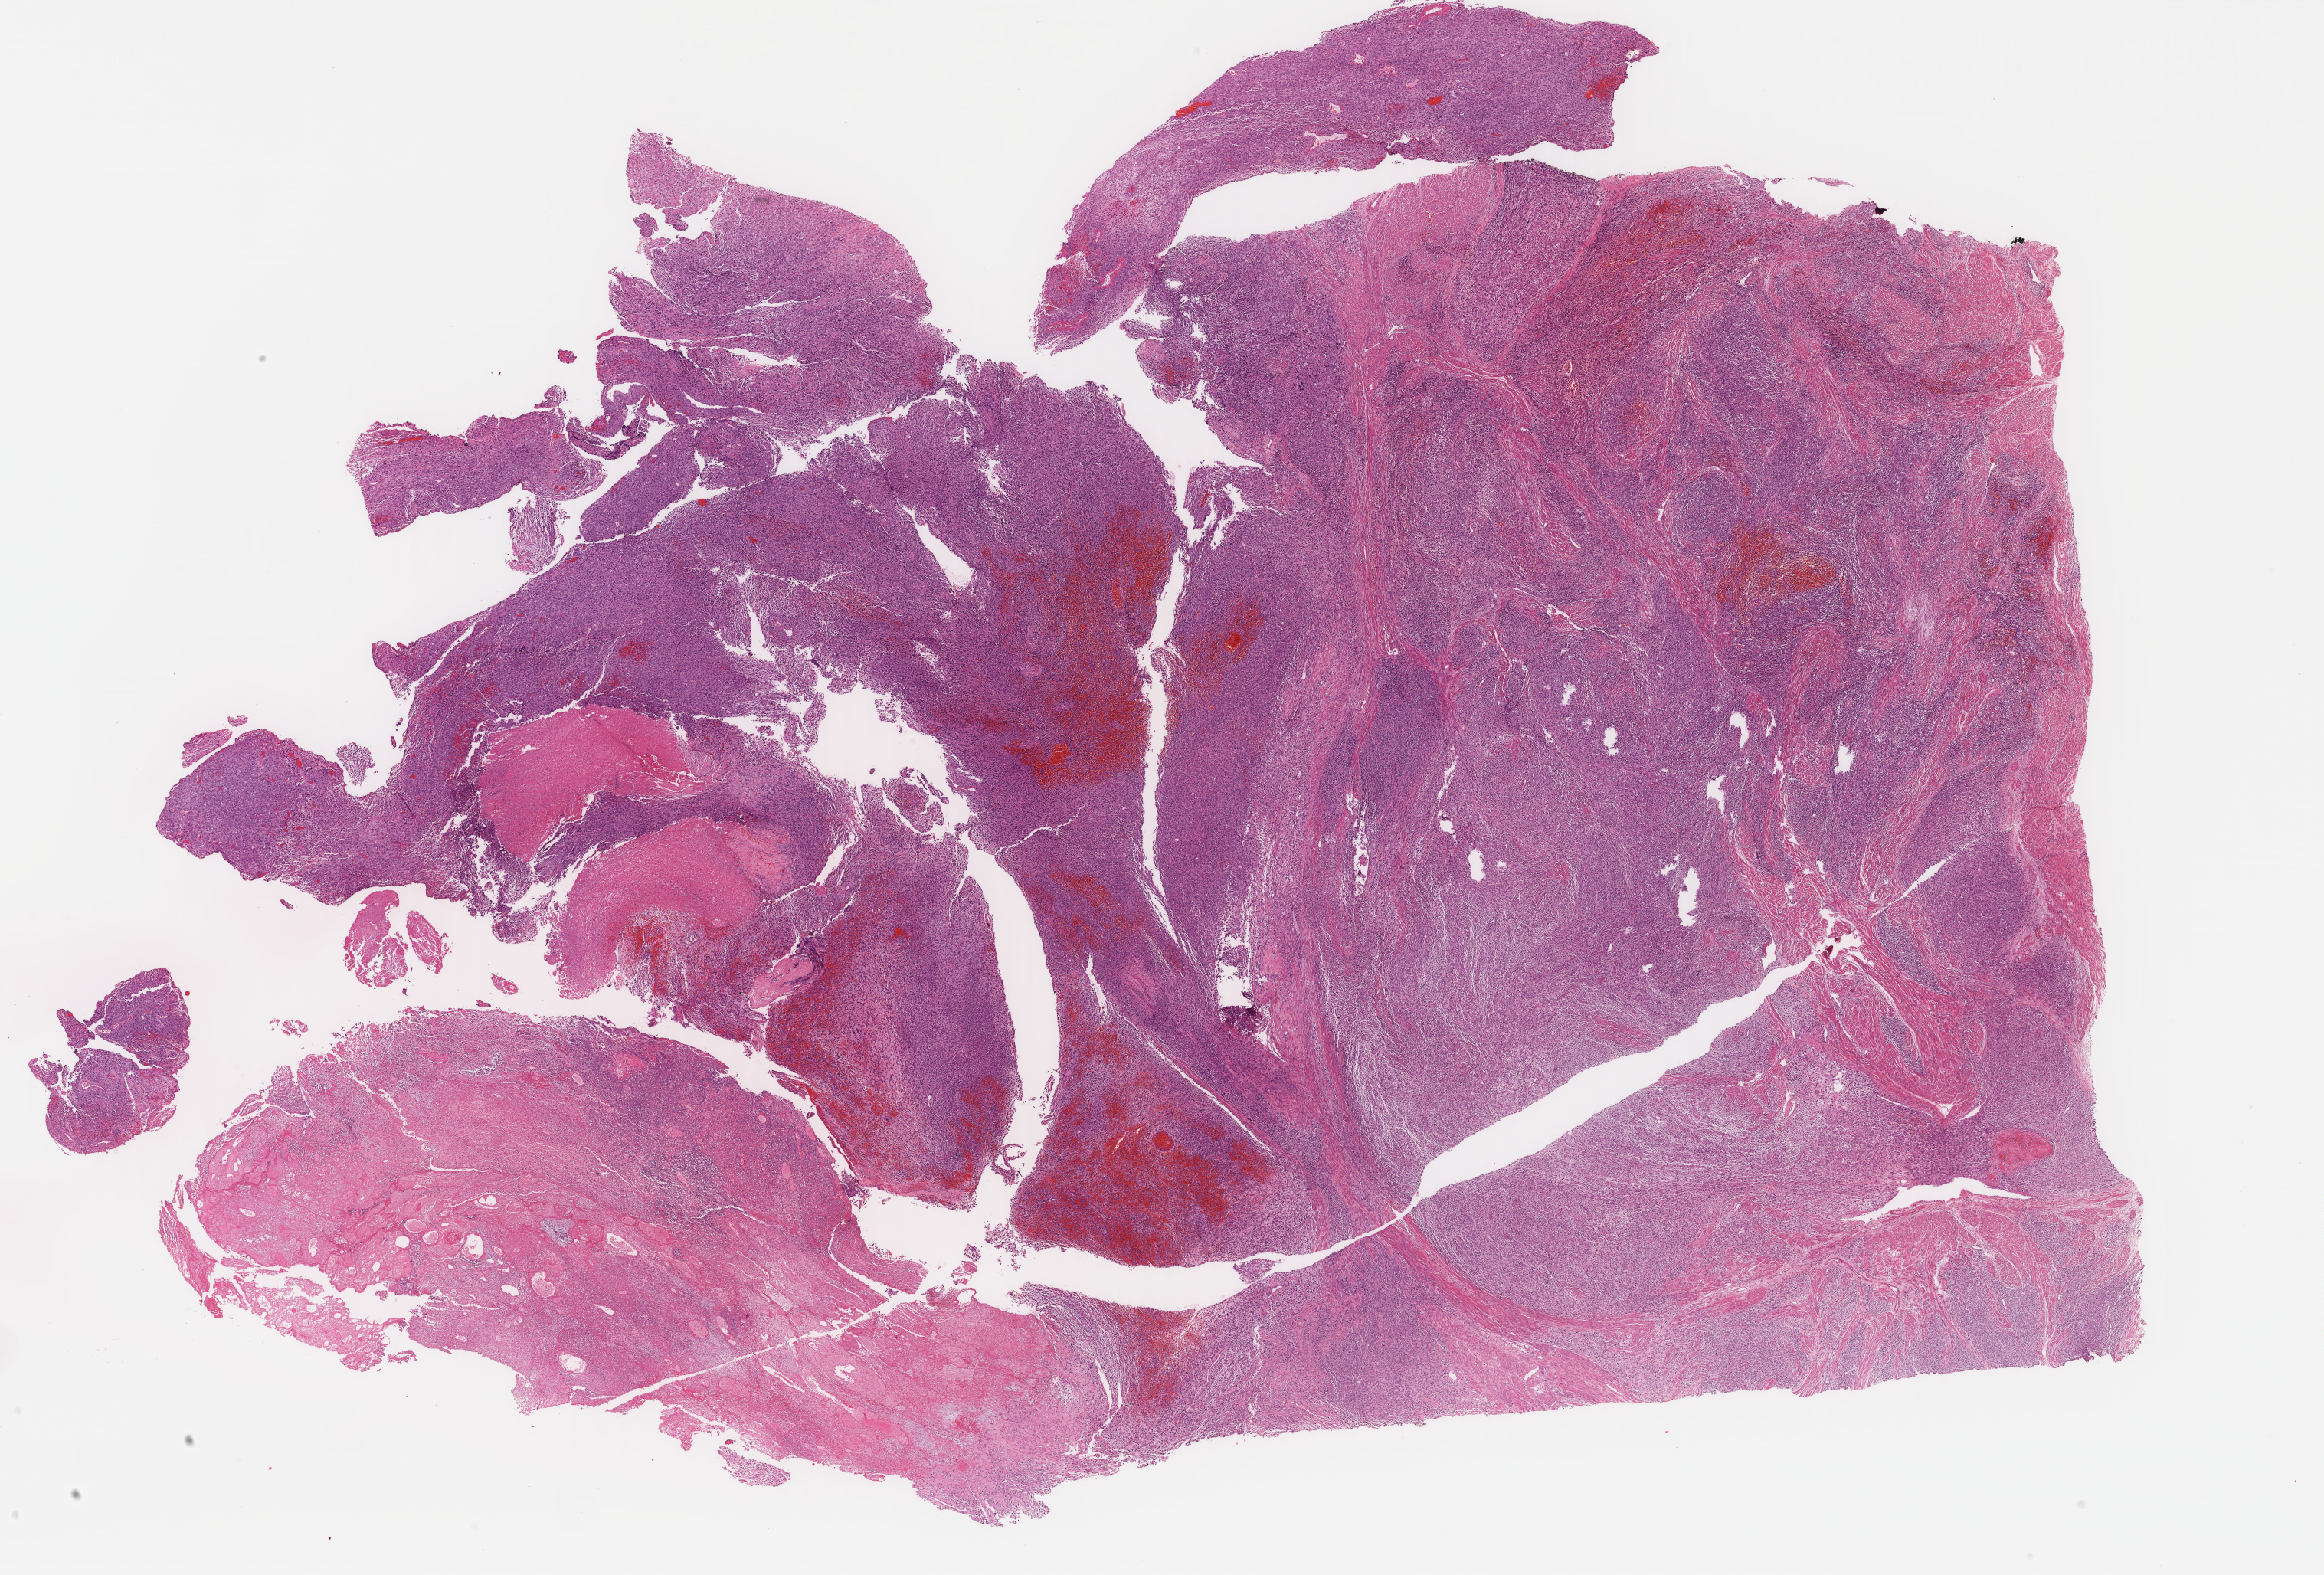
Digitized Hematoxylin and eosin (H&E) stained tissue section (whole slide) — a low-resolution overview of the entire scanned area, about 24.1 x 16.3 mm (slide scanned at 40x); FFPE section; sample: primary tumour, uterus. Patient: female, age at initial diagnosis 41 years. Histologic grade: G3 (poorly differentiated).
FIGO stage: II. Diagnosis: Endometrioid adenocarcinoma, NOS (endometrium). Lymph nodes positive (case pathology): 0 of 11 examined.